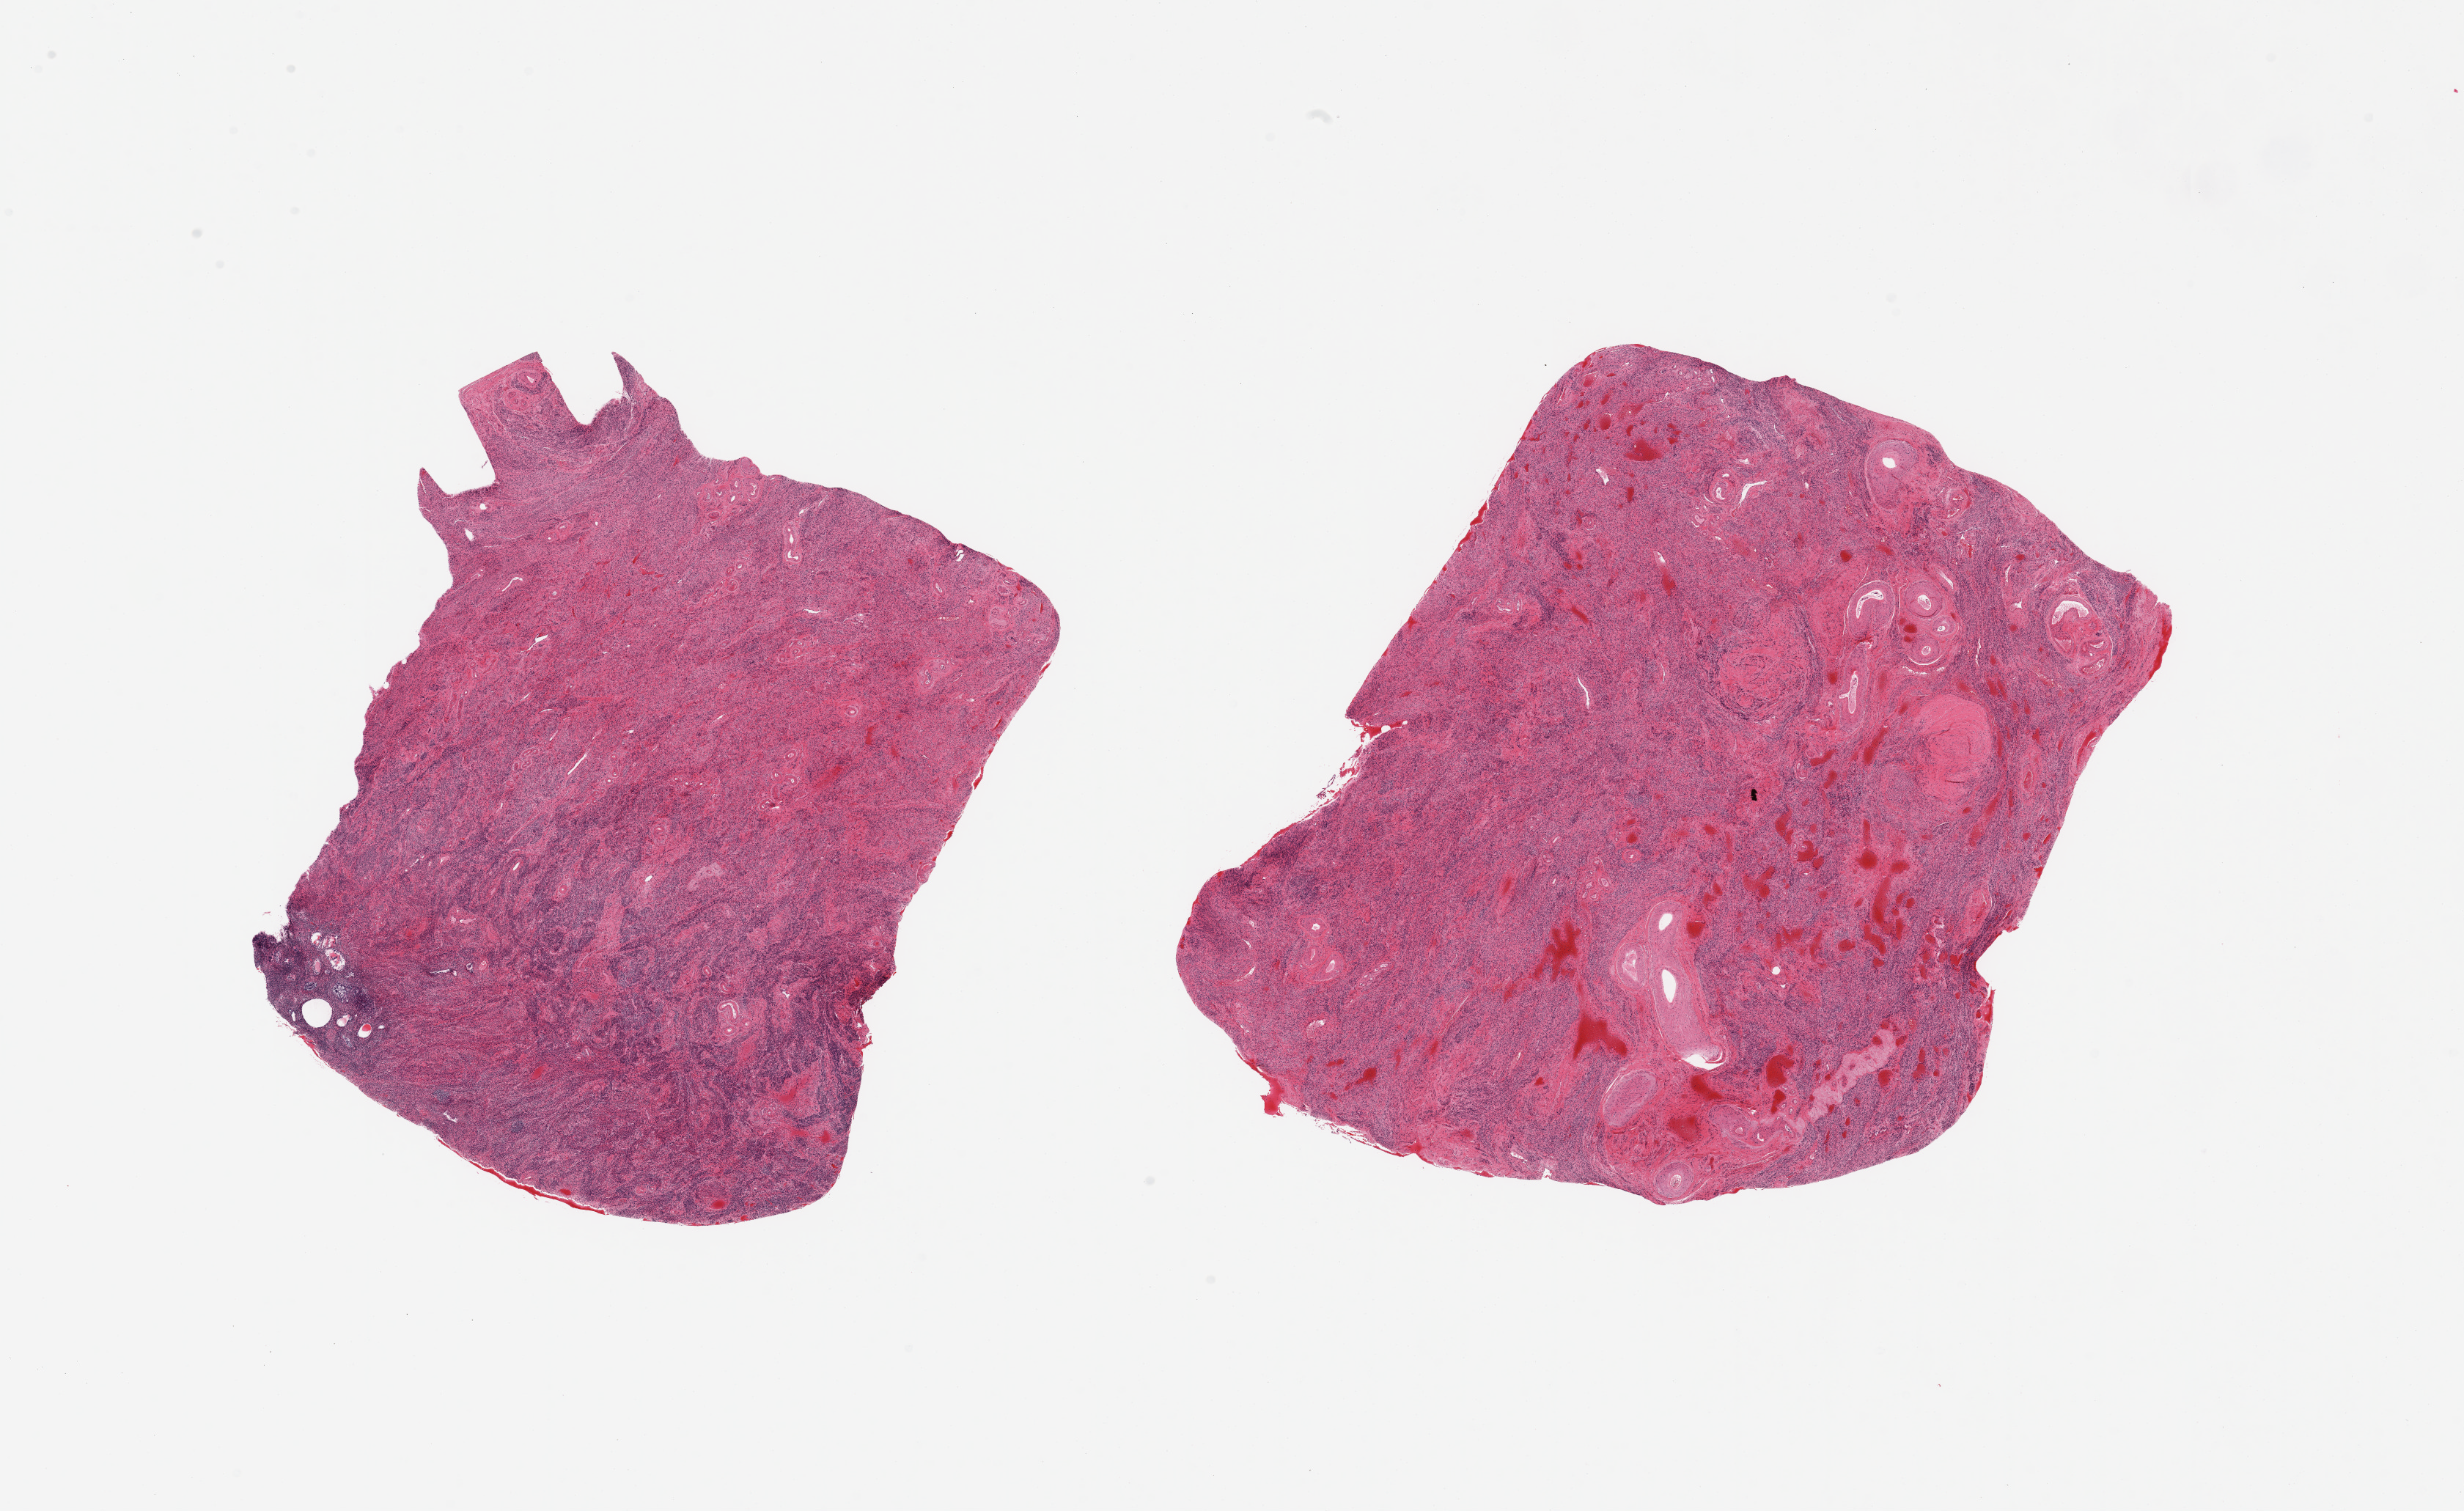
Hematoxylin and eosin (H&E) whole-slide image, whole scanned area (about 26.6 x 16.3 mm) shown as a low-resolution overview. PAXgene-fixed paraffin-embedded (PFPE) section. Target tissue: uterus. Tissue donor sample.
• review note (as recorded): 2 pieces, mainly myometrium; 2mm focus of moderately autolyzed endometrium with trace basalis glands